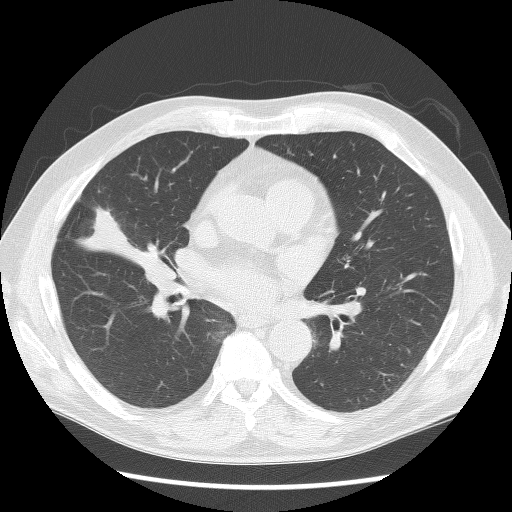
Axial slice from a low-dose chest CT screening exam; third annual screen; lung window (W 1500 / L -600 HU); 120 kVp; slice 71 of 146 in the series; 512 × 512 image matrix, field of view 350 × 350 mm. Male participant, aged 57 years at enrolment. Former smoker at enrolment.
Expert reader's lesion annotation, bounding box [x1, y1, x2, y2] px = [139, 253, 177, 289]. Screening reader's record for this exam (one nodule recorded; not confirmed to be the boxed lesion): non-calcified nodule or mass ≥4 mm, right middle lobe, 19 × 18 mm, smooth margins, soft tissue attenuation, pre-existing on the prior screen: yes; interval growth: yes. Official screen result: positive, other.